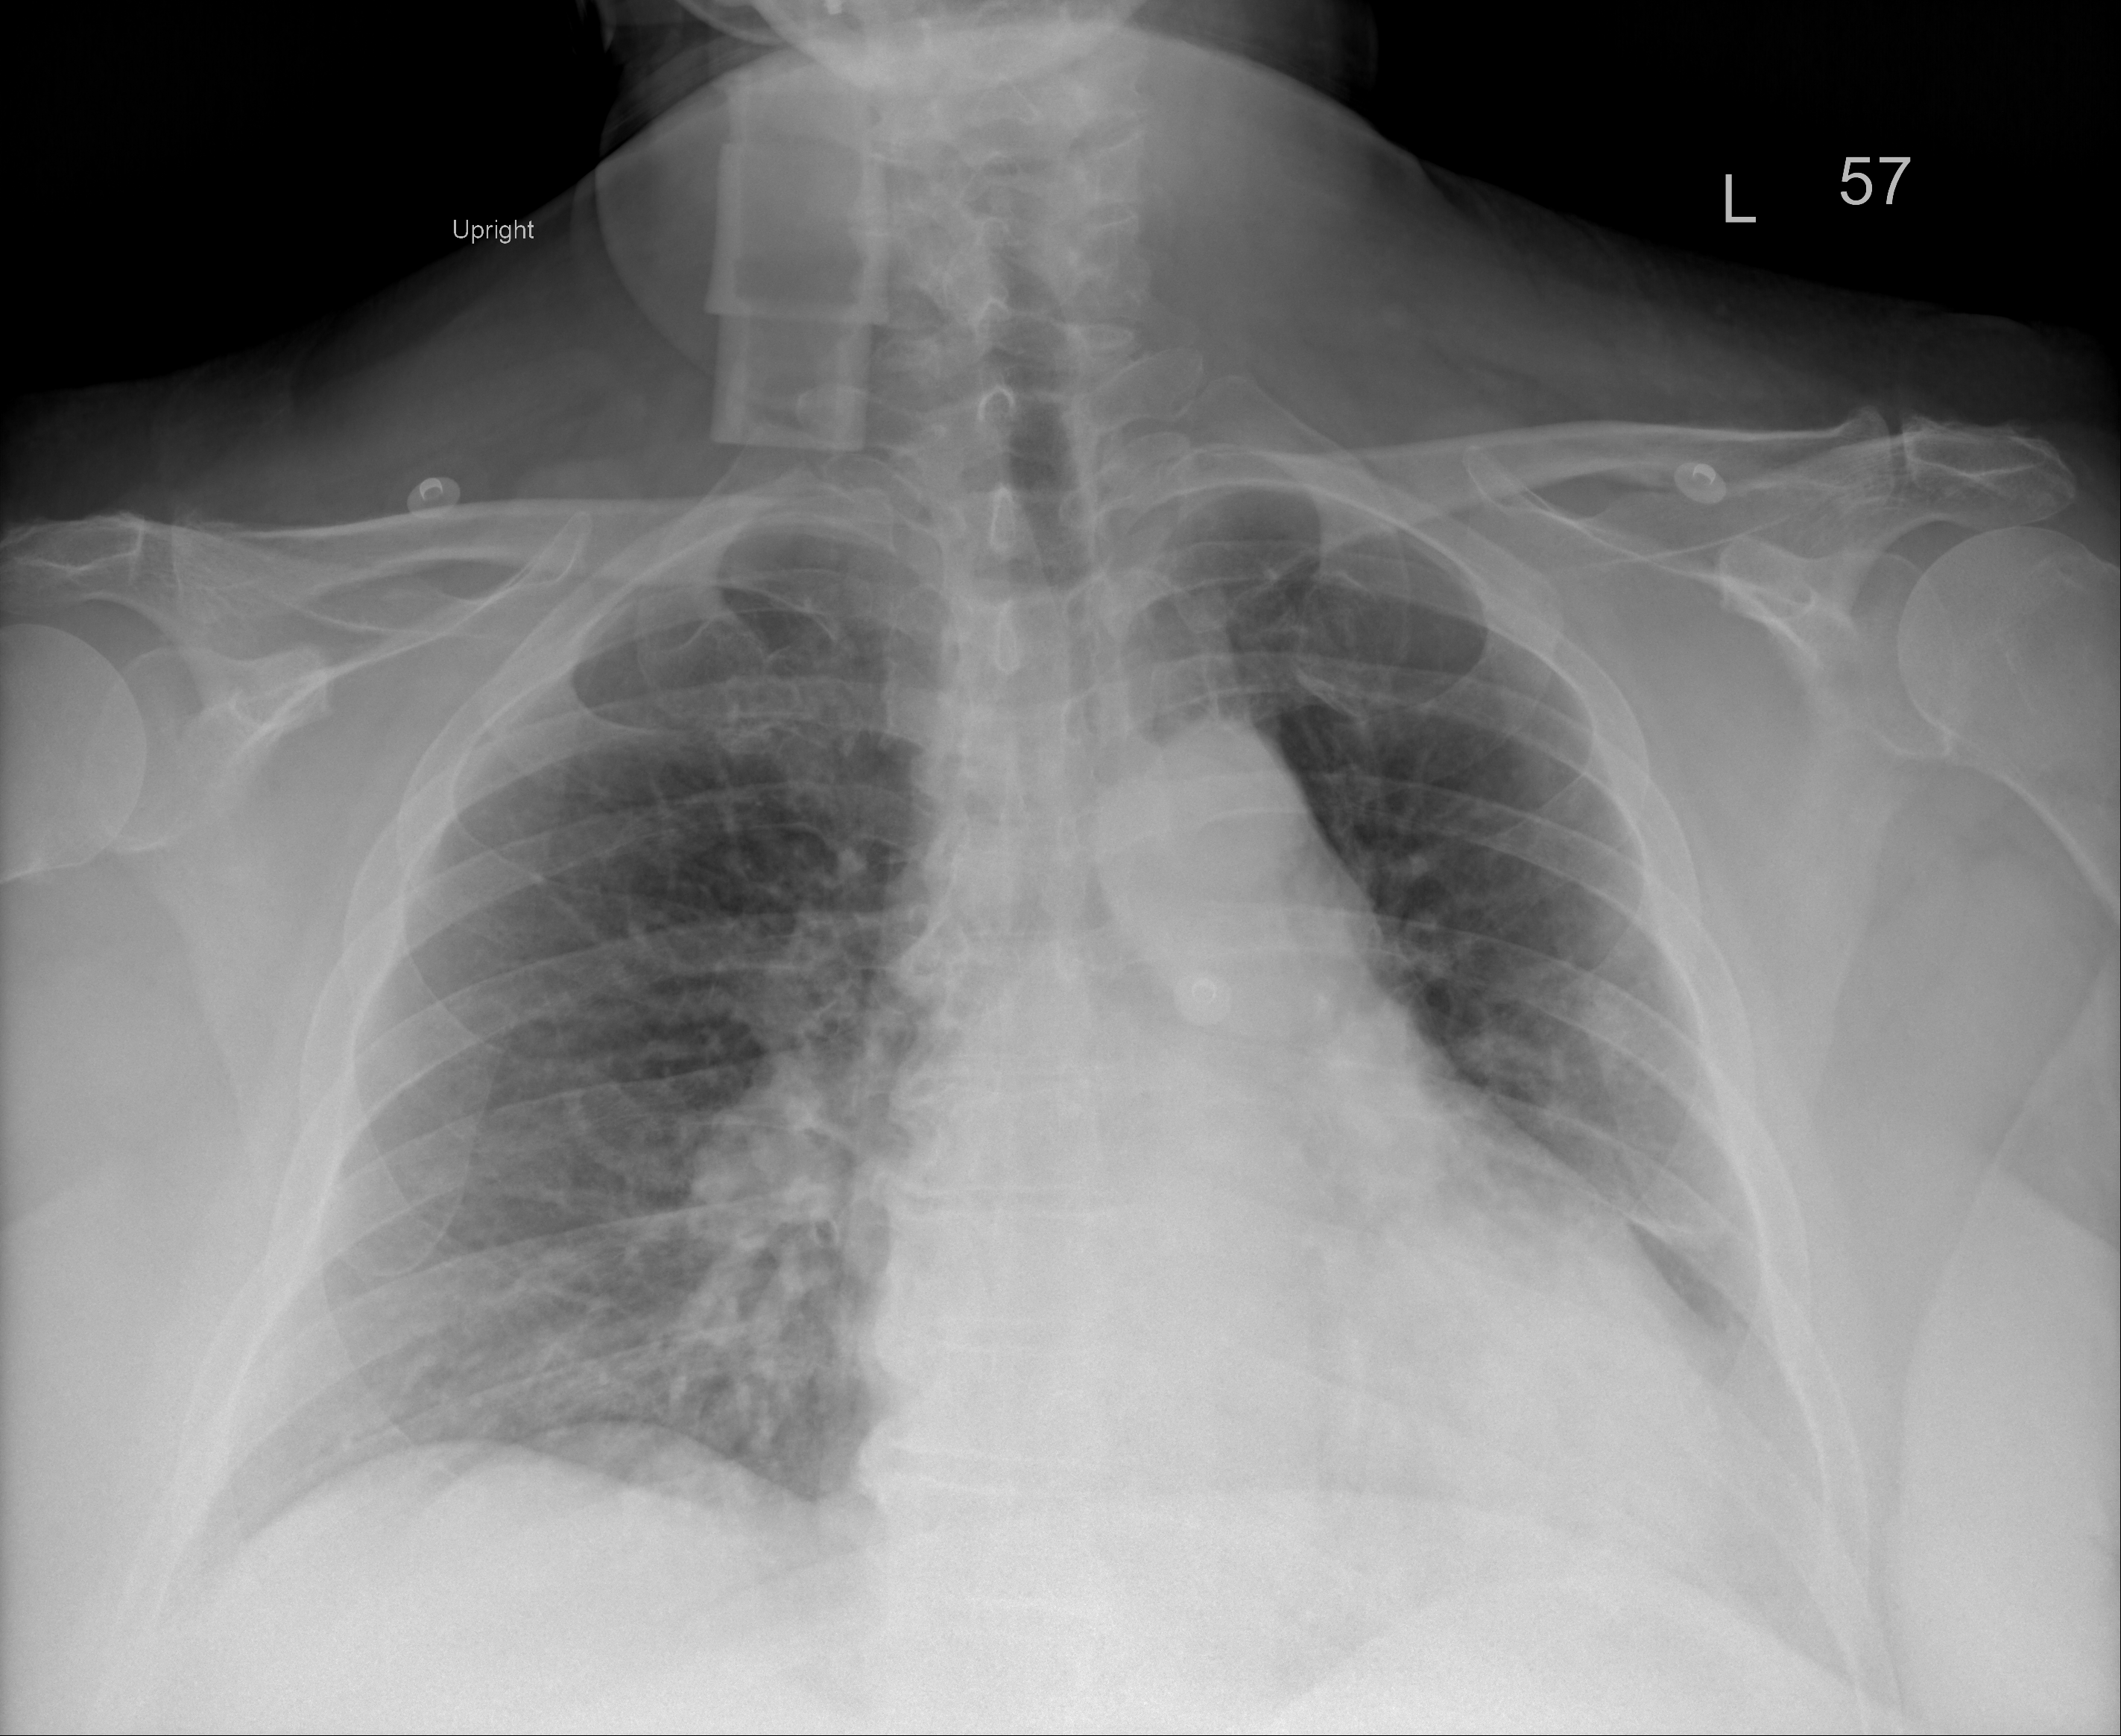
Chest X-ray (portable), AP projection. Female patient, age 59 years; imaged 2 days after the COVID-19 diagnosis.
Key findings recorded by the radiologist: left lower lobe opacity improved but not fully resolved, minimal right infrahilar opacity.